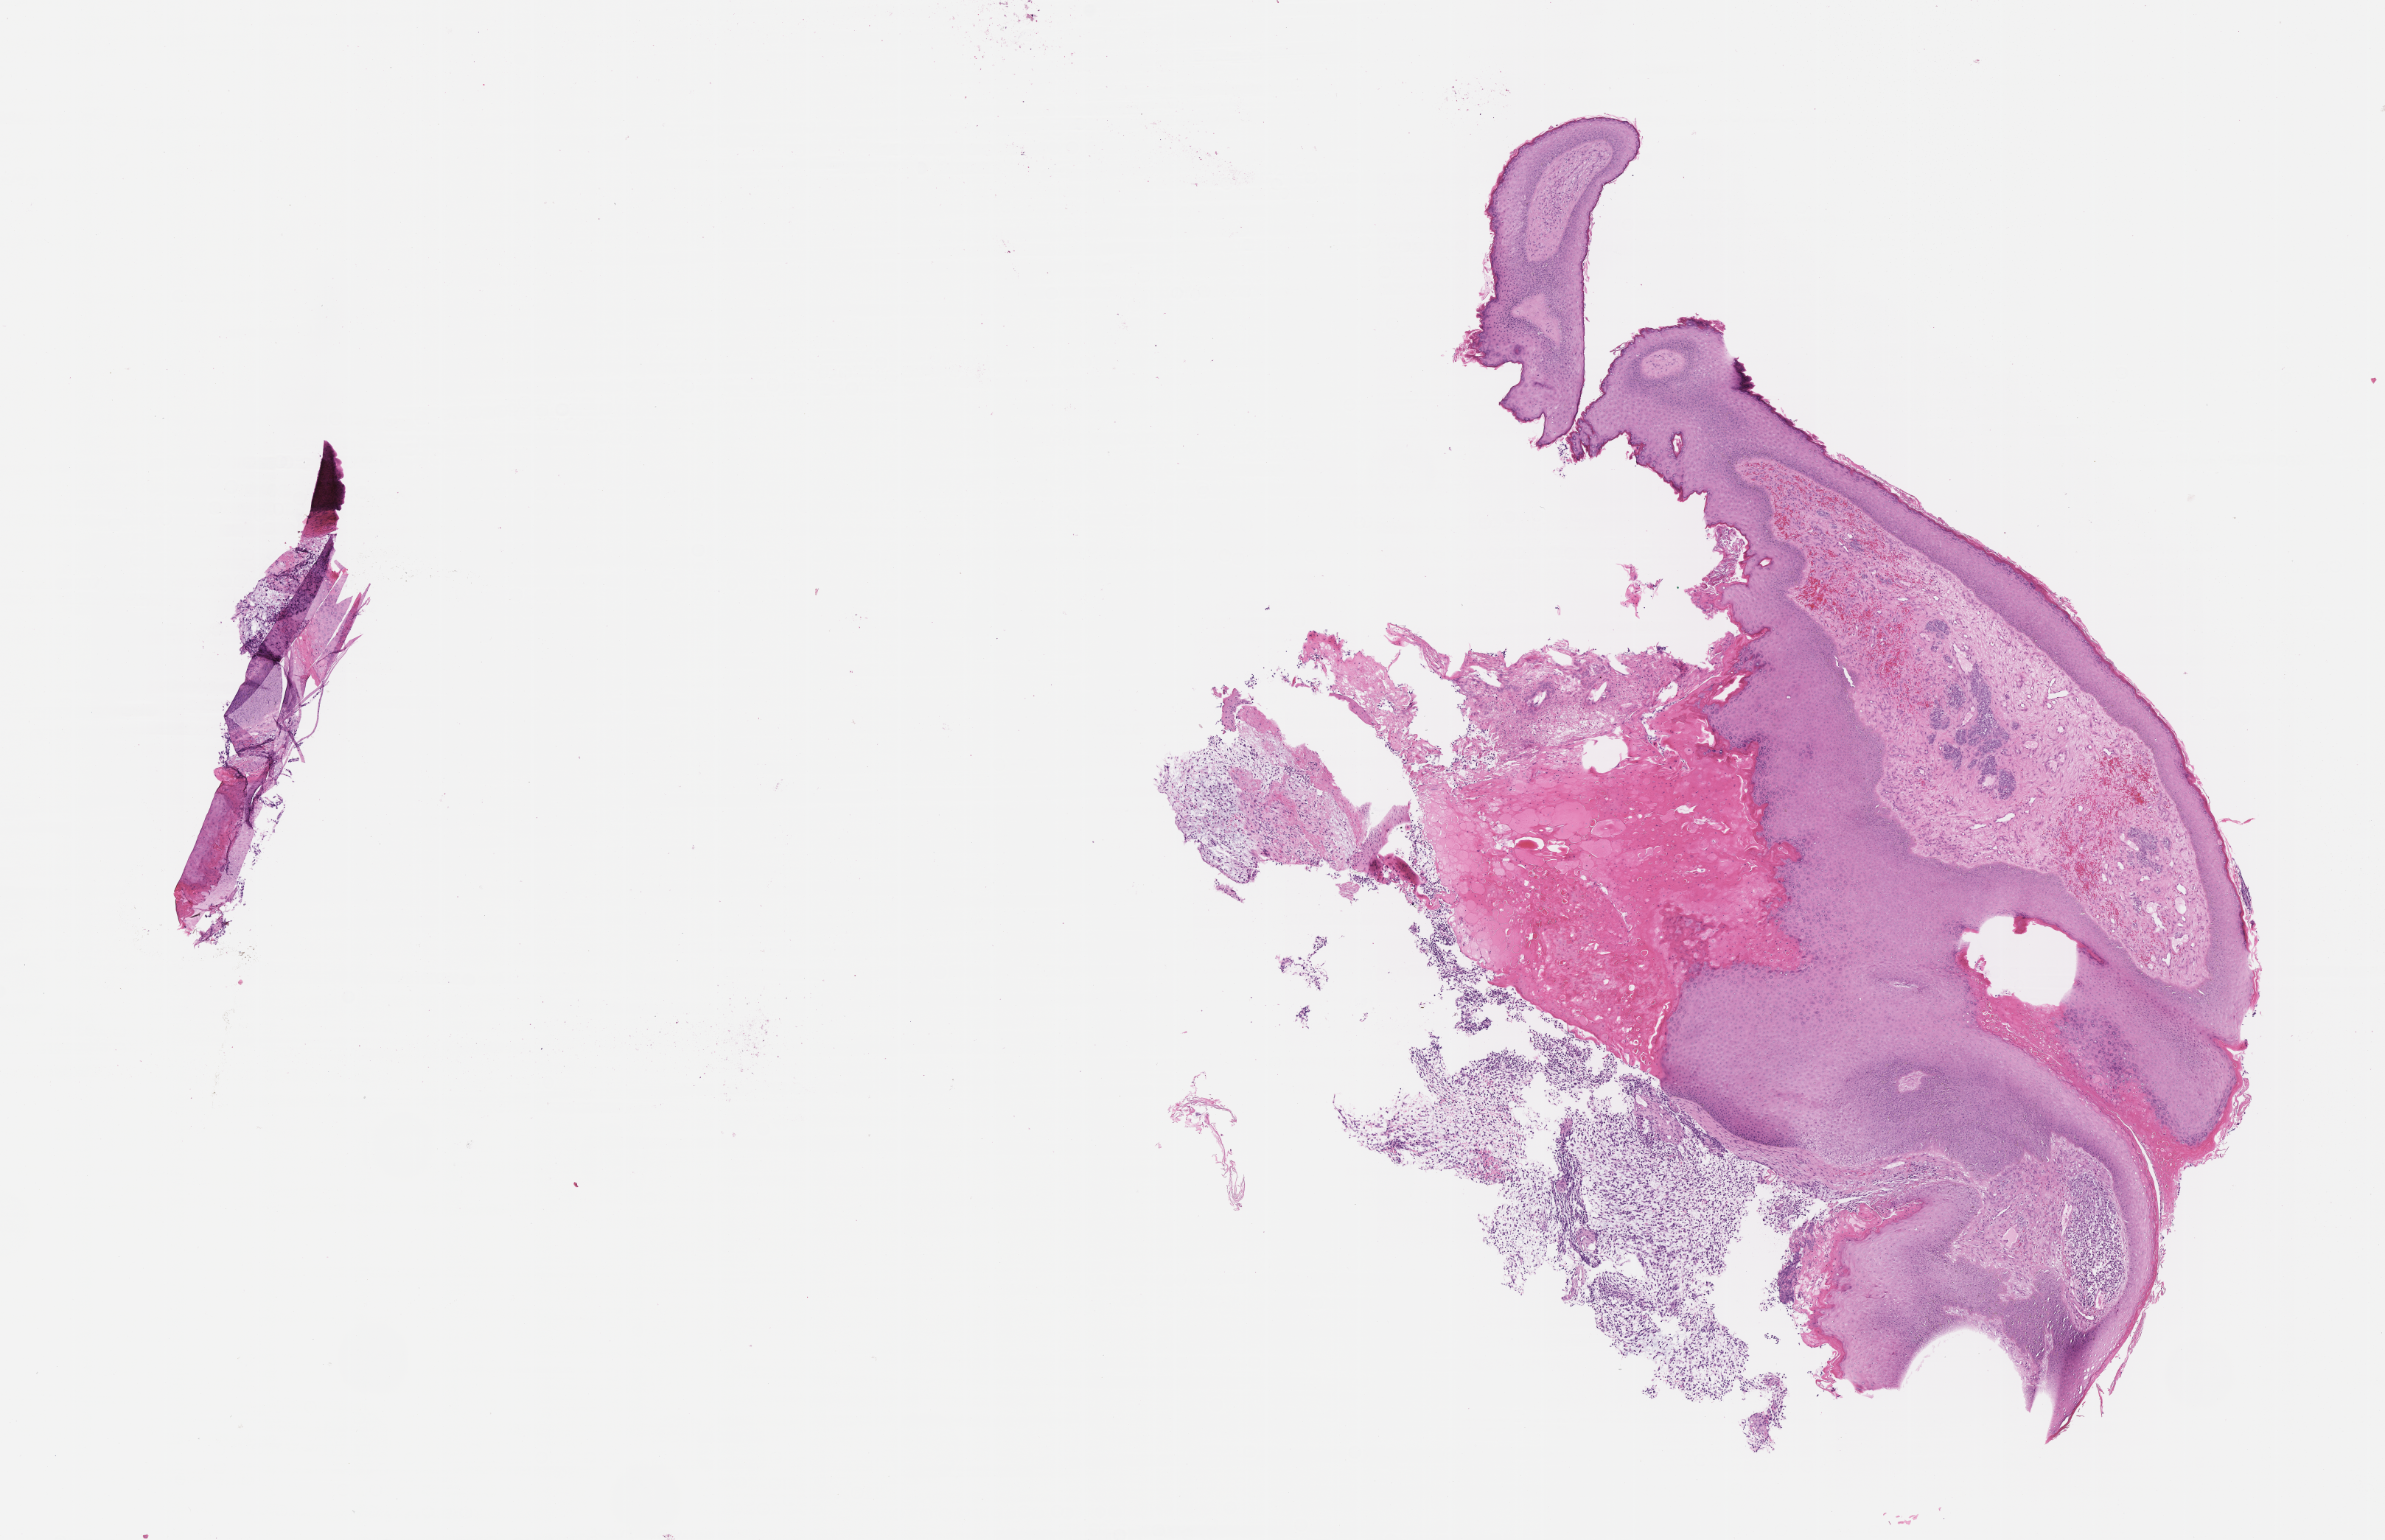
Digitized H&E-stained section of tumor tissue, shown as a low-resolution overview of the whole scanned area (about 13.1 x 8.4 mm); formalin-fixed paraffin-embedded section; site: left ear. Male patient, age at diagnosis 4.6 years.
Diagnosis: rhabdomyosarcoma; histological classification: embryonal rhabdomyosarcoma. Stage (as recorded): 3.